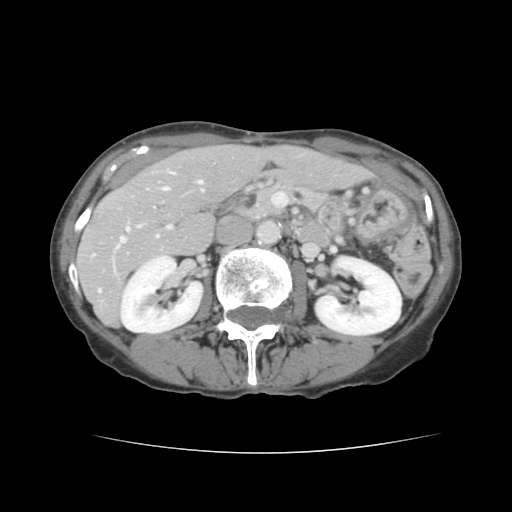
Contrast-enhanced abdominal CT, one axial slice. Position 64 of 136 along the scan axis. 120 kVp. Intravenous contrast given. Soft-tissue window (W 400 / L 40 HU). 2.5 mm slice thickness. 512 × 512 image matrix, field of view 319 × 319 mm. Female patient, age 77 years. Case-level facts recorded for this patient, not image findings: diagnosis: colorectal cancer liver metastases, imaged before liver resection; multiple liver metastases: yes; largest metastasis: 3 cm; disease in both lobes: no.
Structures marked on this image (outlined manually by an expert reader):
- hepatic veins: bounding box [x1, y1, x2, y2] px = [117, 172, 203, 248]
- liver: [78, 146, 369, 324]
- planned liver remnant (the part of the liver to remain after resection): [162, 146, 369, 206]
- portal vein (with intrahepatic branches): [98, 225, 172, 292]